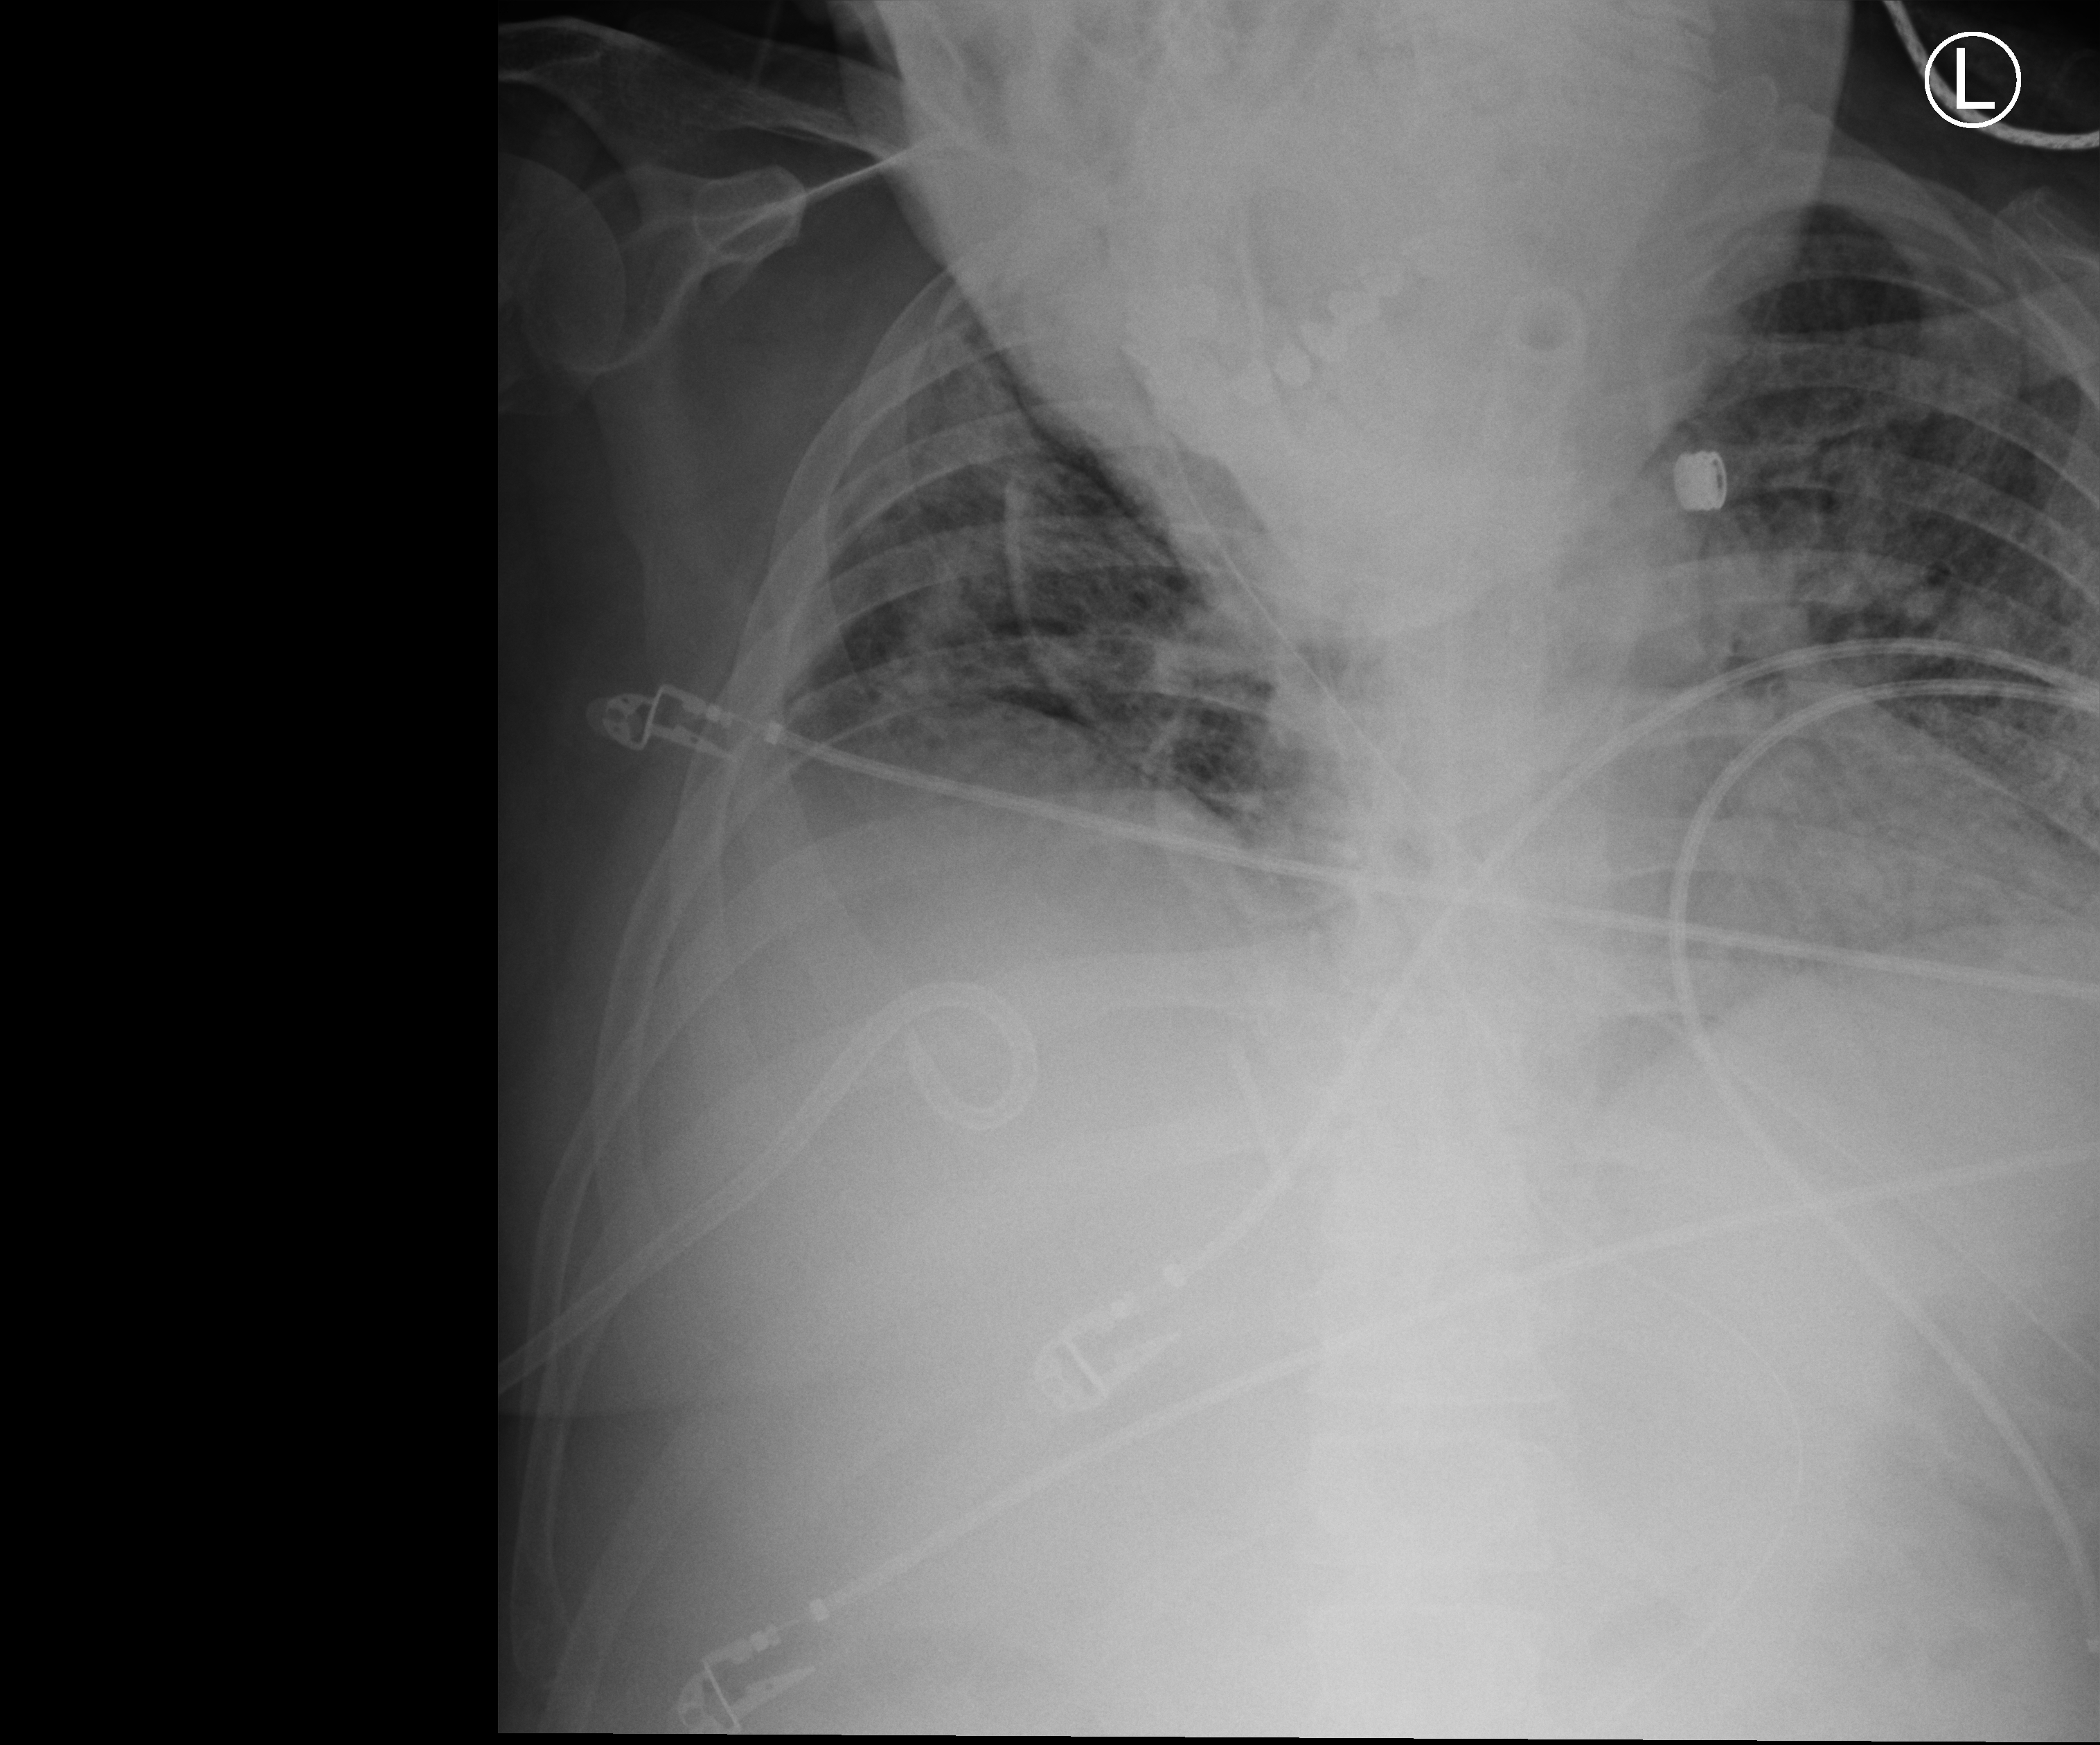
Chest X-ray (portable); anteroposterior (AP) projection. Male patient hospitalised with COVID-19, age 18–59 years.
Admission-level facts for this patient (not findings on this image; timing relative to this image not recorded):
- mechanically ventilated during this hospital stay: yes
- hypertension (admission record): yes
- admitted to intensive care during this hospital stay: yes